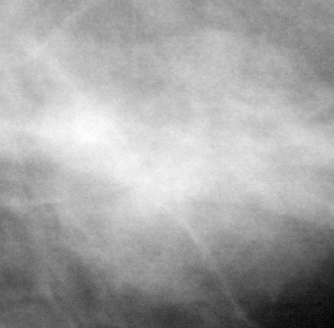
Region of interest cut from a scanned film mammogram (one marked finding), left breast, MLO view.
Mass, shape round, margins circumscribed; BI-RADS assessment category 4; subtlety rating 3 on a 1 (subtle) to 5 (obvious) scale; pathology result (as recorded, not read from the image): benign.